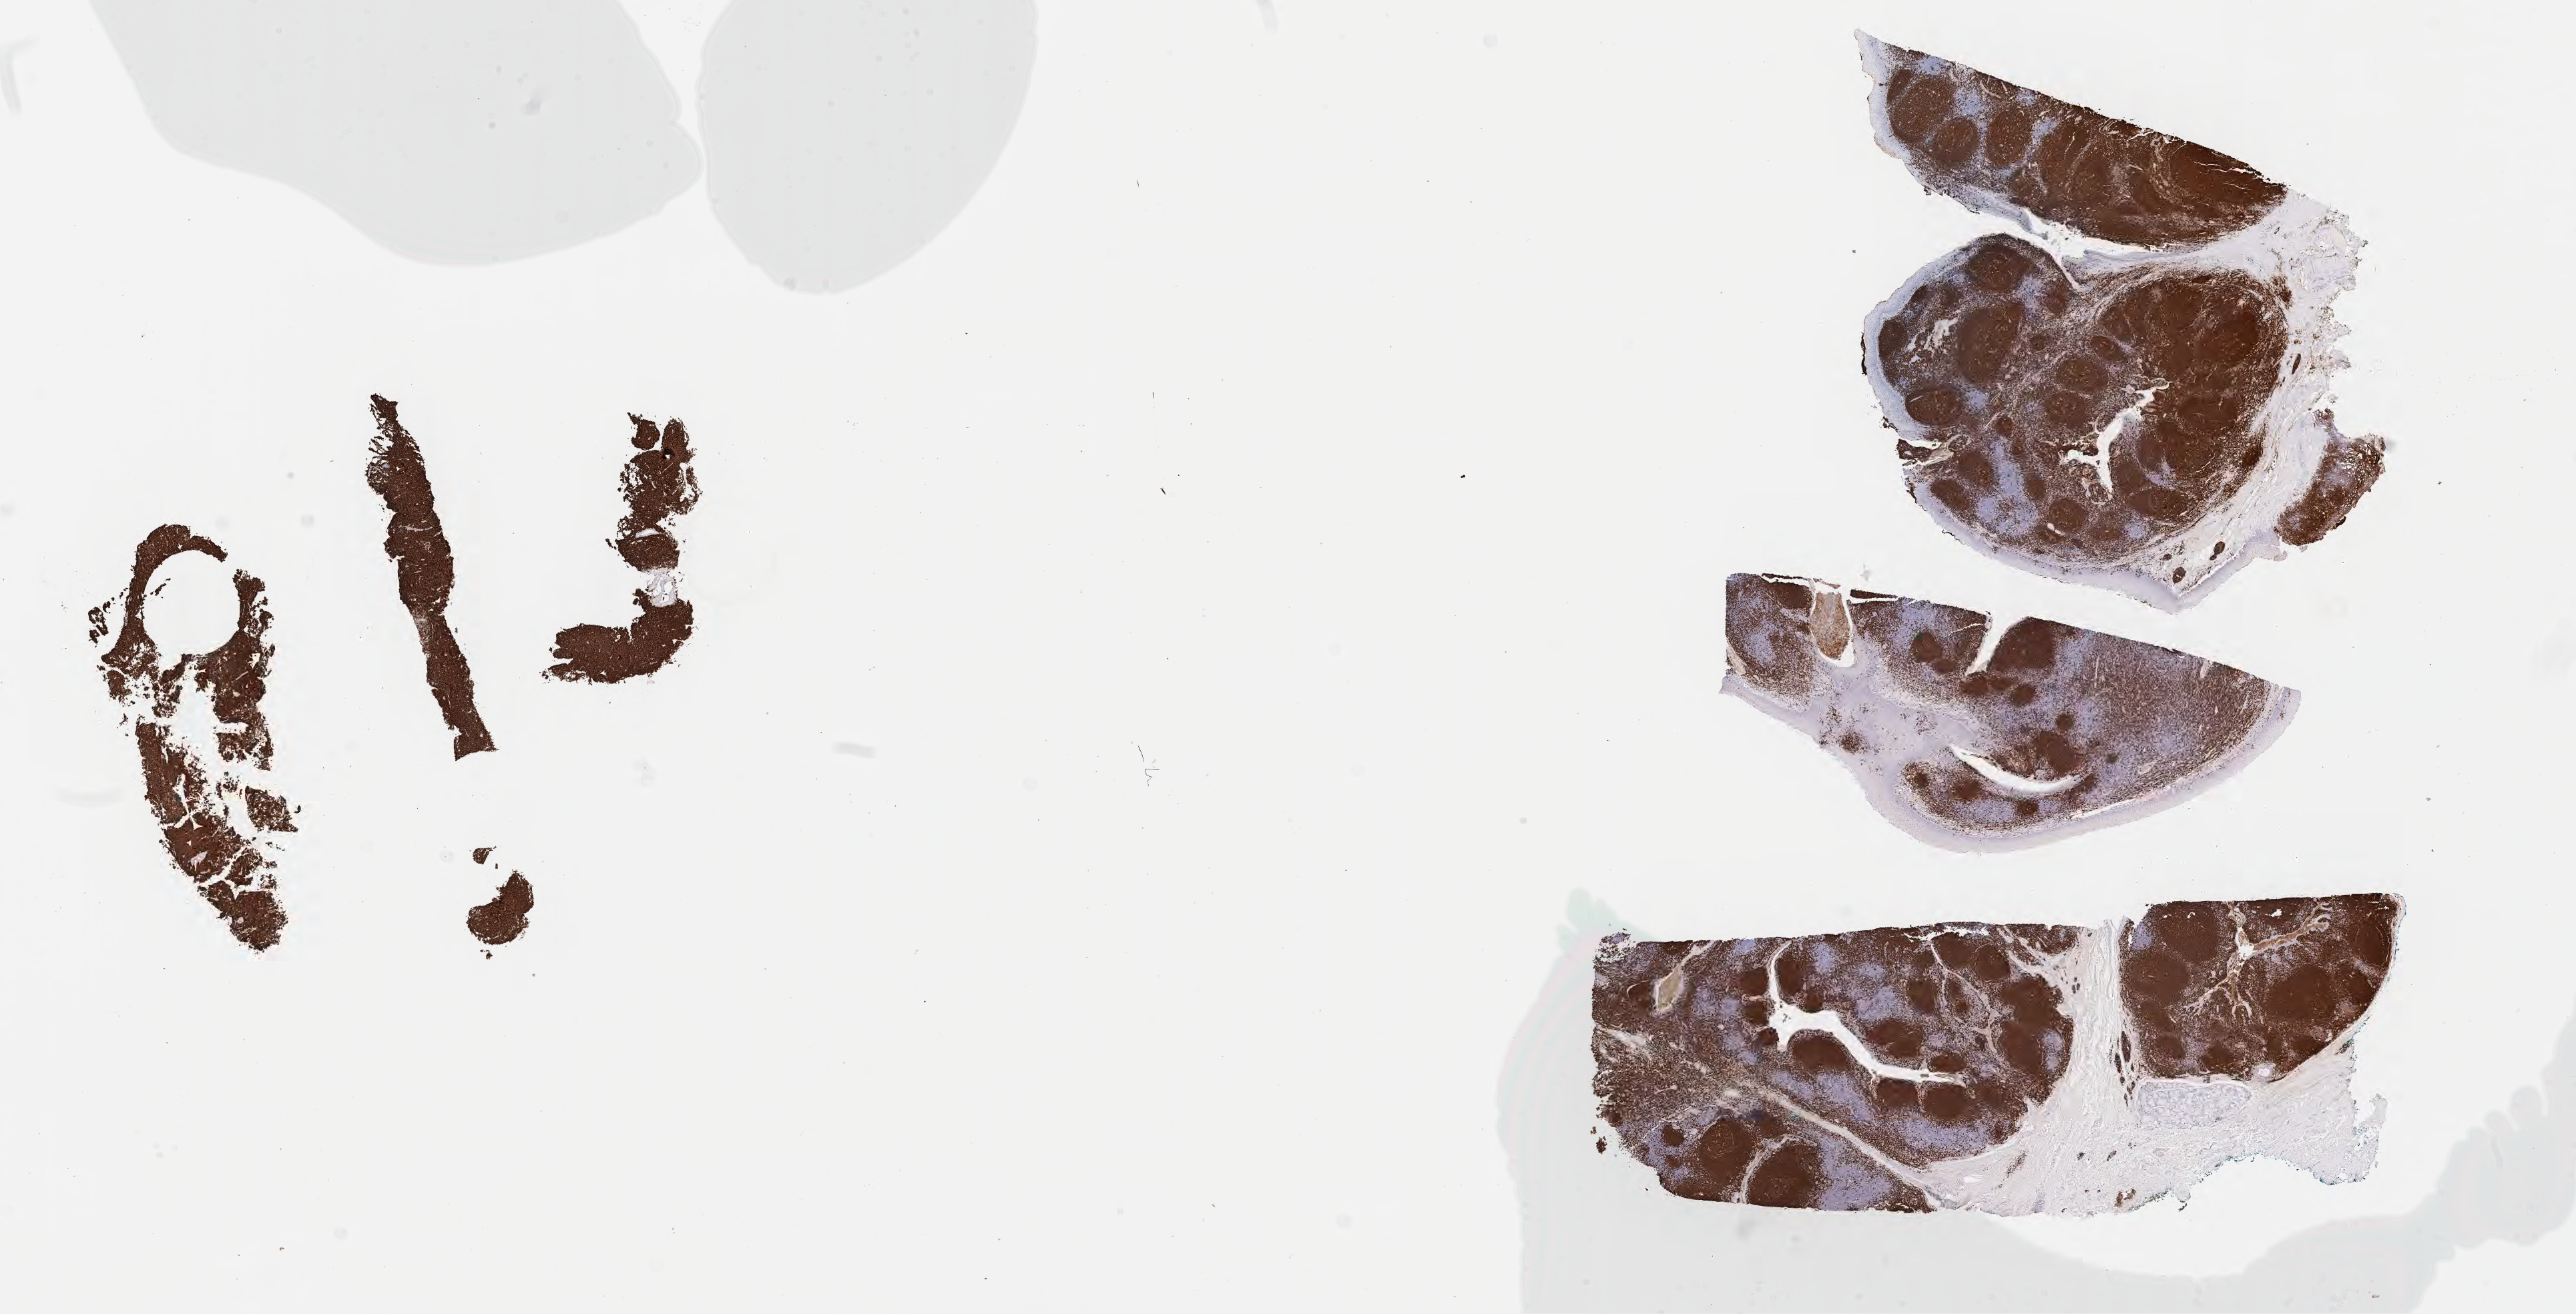
IHC for CD20, whole-slide image, a low-resolution overview of the entire scanned area, about 31.2 x 15.9 mm. Specimen: tumor tissue. Site: spleen. Male patient; age at initial diagnosis 8 years.
Histologic diagnosis: Burkitt lymphoma, NOS.